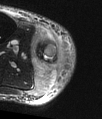
MRI of an extremity soft-tissue mass, one axial slice. Position 16 of 48 along the scan axis. T2-weighted fat-saturated. MR volume resampled by the dataset authors to the PET/CT grid (not the native acquisition matrix). 3.27 mm slice thickness. 102 × 119 image matrix, field of view 100 × 116 mm. Male patient. Case-level facts recorded for this patient, not image findings: histological type: pleiomorphic liposarcoma; grade: high; site of the primary tumour: right calf.
Annotated regions visible in this slice (expert contour drawn on MRI and transferred to this co-registered scan by the dataset authors):
- gross tumour volume including surrounding oedema: bounding box (x1, y1, x2, y2) in pixels: (32, 30, 65, 93)
- gross tumour volume (mass): (37, 42, 59, 66)